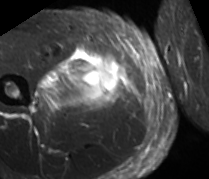
MRI of an extremity soft-tissue mass, one axial slice; position 30 of 89 along the scan axis; STIR; MR volume resampled by the dataset authors to the PET/CT grid (not the native acquisition matrix); 209 × 179 image matrix, field of view 204 × 175 mm. Male patient. From the clinical record (not read from this slice): histological type: undifferentiated - pleiomorphic; grade: high; site of the primary tumour: right thigh.
Annotated regions visible in this slice (expert contour drawn on MRI and transferred to this co-registered scan by the dataset authors):
- gross tumour volume including surrounding oedema: box from (x=32, y=46) to (x=122, y=111) px
- gross tumour volume (mass): (x=69, y=57)–(x=122, y=102)